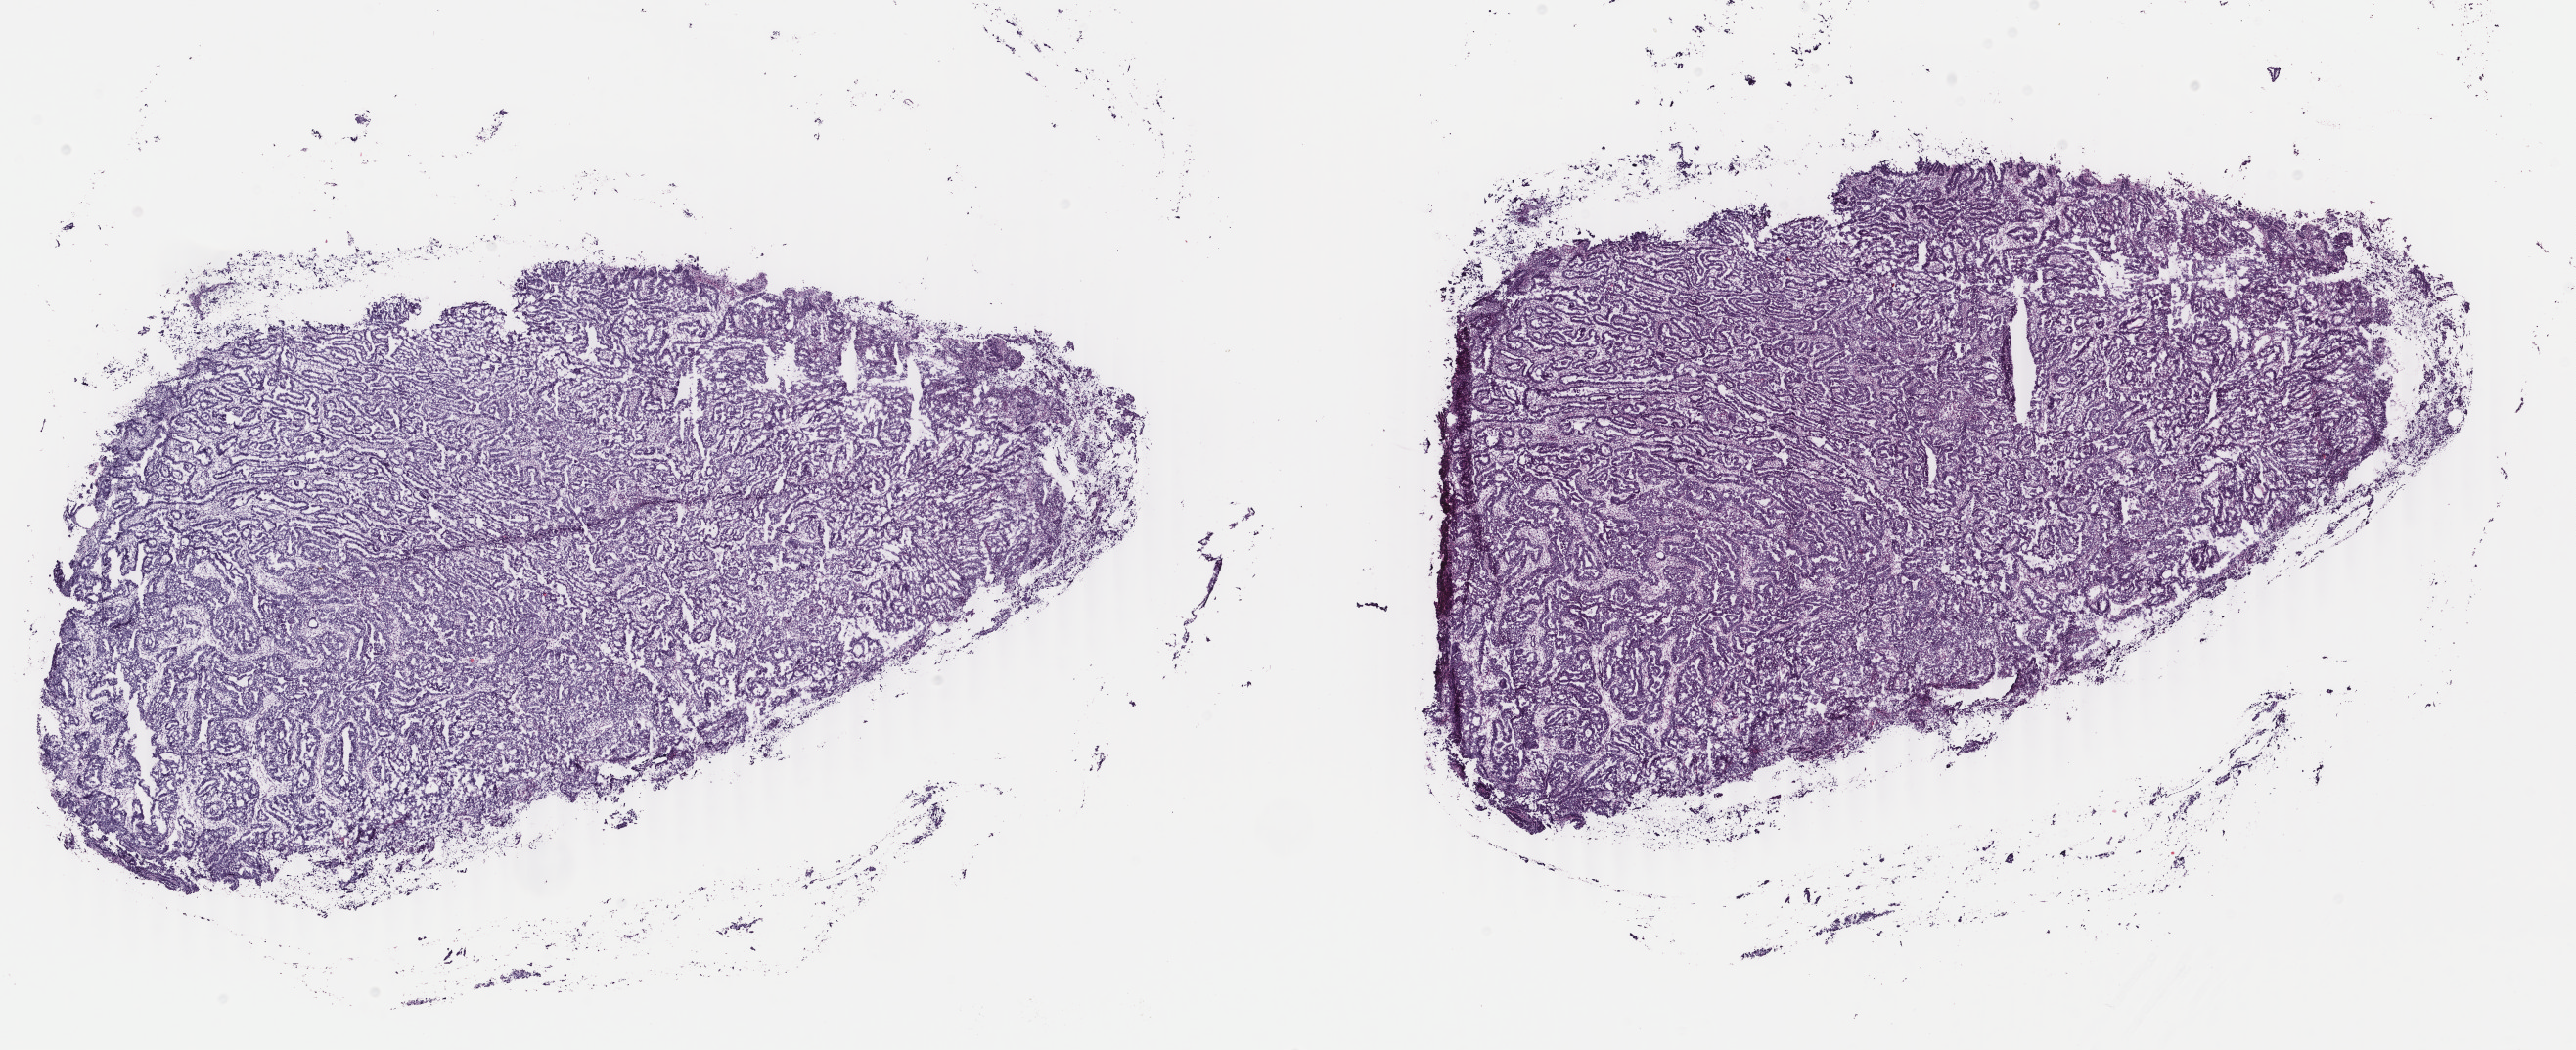
Hematoxylin and eosin (H&E) stained whole-slide image — whole scanned area (about 20.9 x 8.5 mm, slide scanned at 40x) shown as a low-resolution overview. Frozen section from the bottom of the tissue portion. Sample: primary tumour, uterus. Female, age 59 years at initial diagnosis. Histologic grade: G3 (poorly differentiated). Pathologist review of this section (percent, as recorded): tumour cells 80%, tumour nuclei 90%, normal cells 0%, stromal cells 10%, necrosis 10%. Inflammatory infiltration, as recorded: lymphocyte infiltration 10%, monocyte infiltration 0%, neutrophil infiltration 10%.
FIGO stage: IVA. Diagnosis: Serous cystadenocarcinoma, NOS.